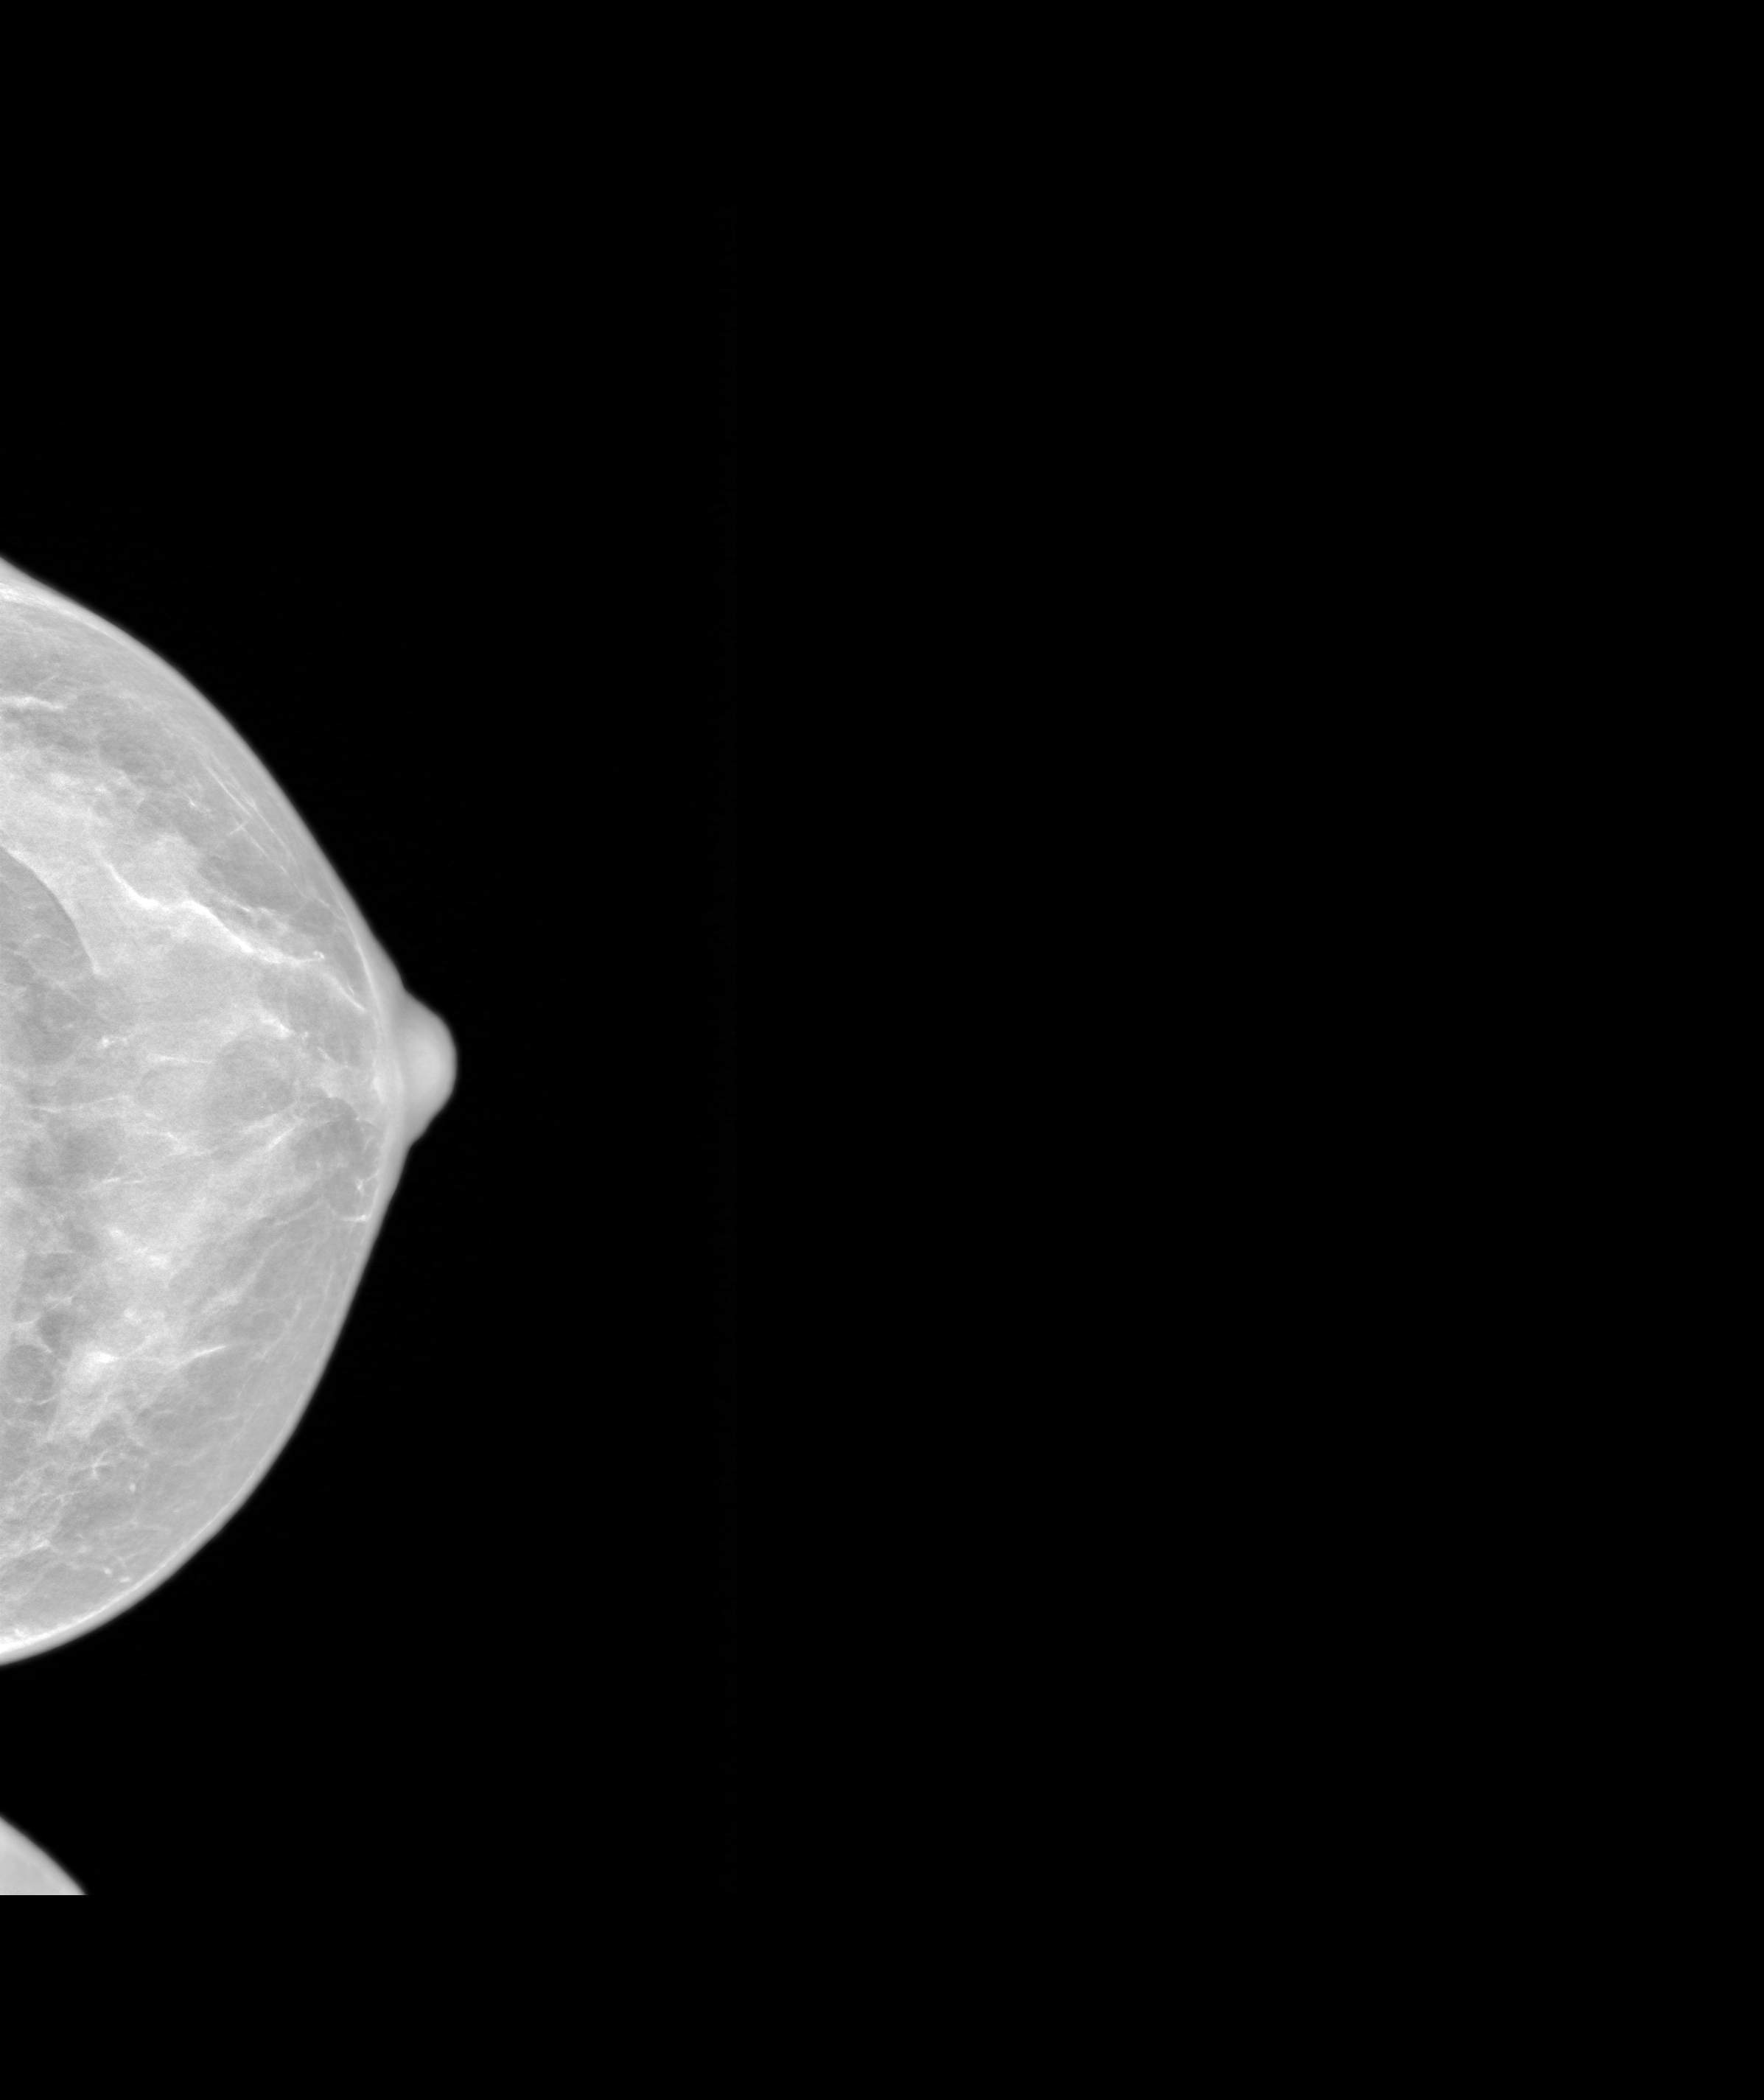
Annual screening mammography examination. Patient: female, 47 years.
Image type: synthesized 2-D view from tomosynthesis. Breast: left. Projection: cranio-caudal projection.